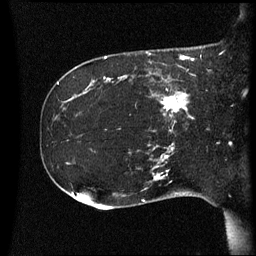
Breast MRI (dynamic contrast-enhanced), one sagittal slice; position 16 of 60 along the scan axis; dynamic contrast-enhanced series, image 2 of 3 at this slice position (ordered by acquisition); 1.5 T; TE 4.2 ms, TR 8.4 ms; 2.2 mm slice thickness; 256 × 256 image matrix, field of view 220 × 220 mm. Patient: female, 41 years. Case-level facts recorded for this patient, not image findings: setting: breast cancer imaged before/during neoadjuvant chemotherapy; receptor status: HER2-positive.
Structures marked on this image (semi-automatically segmented with operator editing):
- analysis volume of interest (the breast-tissue region the enhancement analysis was run in; not a lesion): box from (x=122, y=80) to (x=197, y=123) px
- tumour enhancement mask (voxels above the 70 % enhancement threshold inside the analysis volume of interest): (x=162, y=92)–(x=190, y=117)